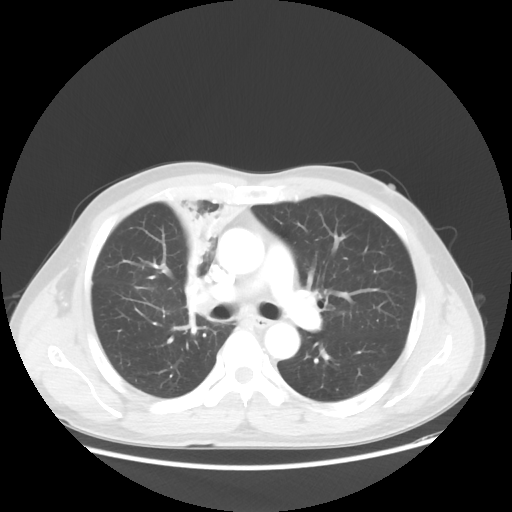
Chest CT, one axial slice; position 33 of 56 along the scan axis; reconstruction kernel STANDARD; 100 kVp; lung window (W 1500 / L -600 HU); 5 mm slice thickness; 512 × 512 image matrix. Patient: male, 60 years. From the clinical record (not read from this slice): clinical TNM (as recorded): T2a N1 M0.
Annotated regions visible in this slice (rectangle marked by the reading radiologist):
- lung tumour (recorded histology: squamous cell carcinoma): bounding box (x1, y1, x2, y2) in pixels: (160, 187, 239, 323)